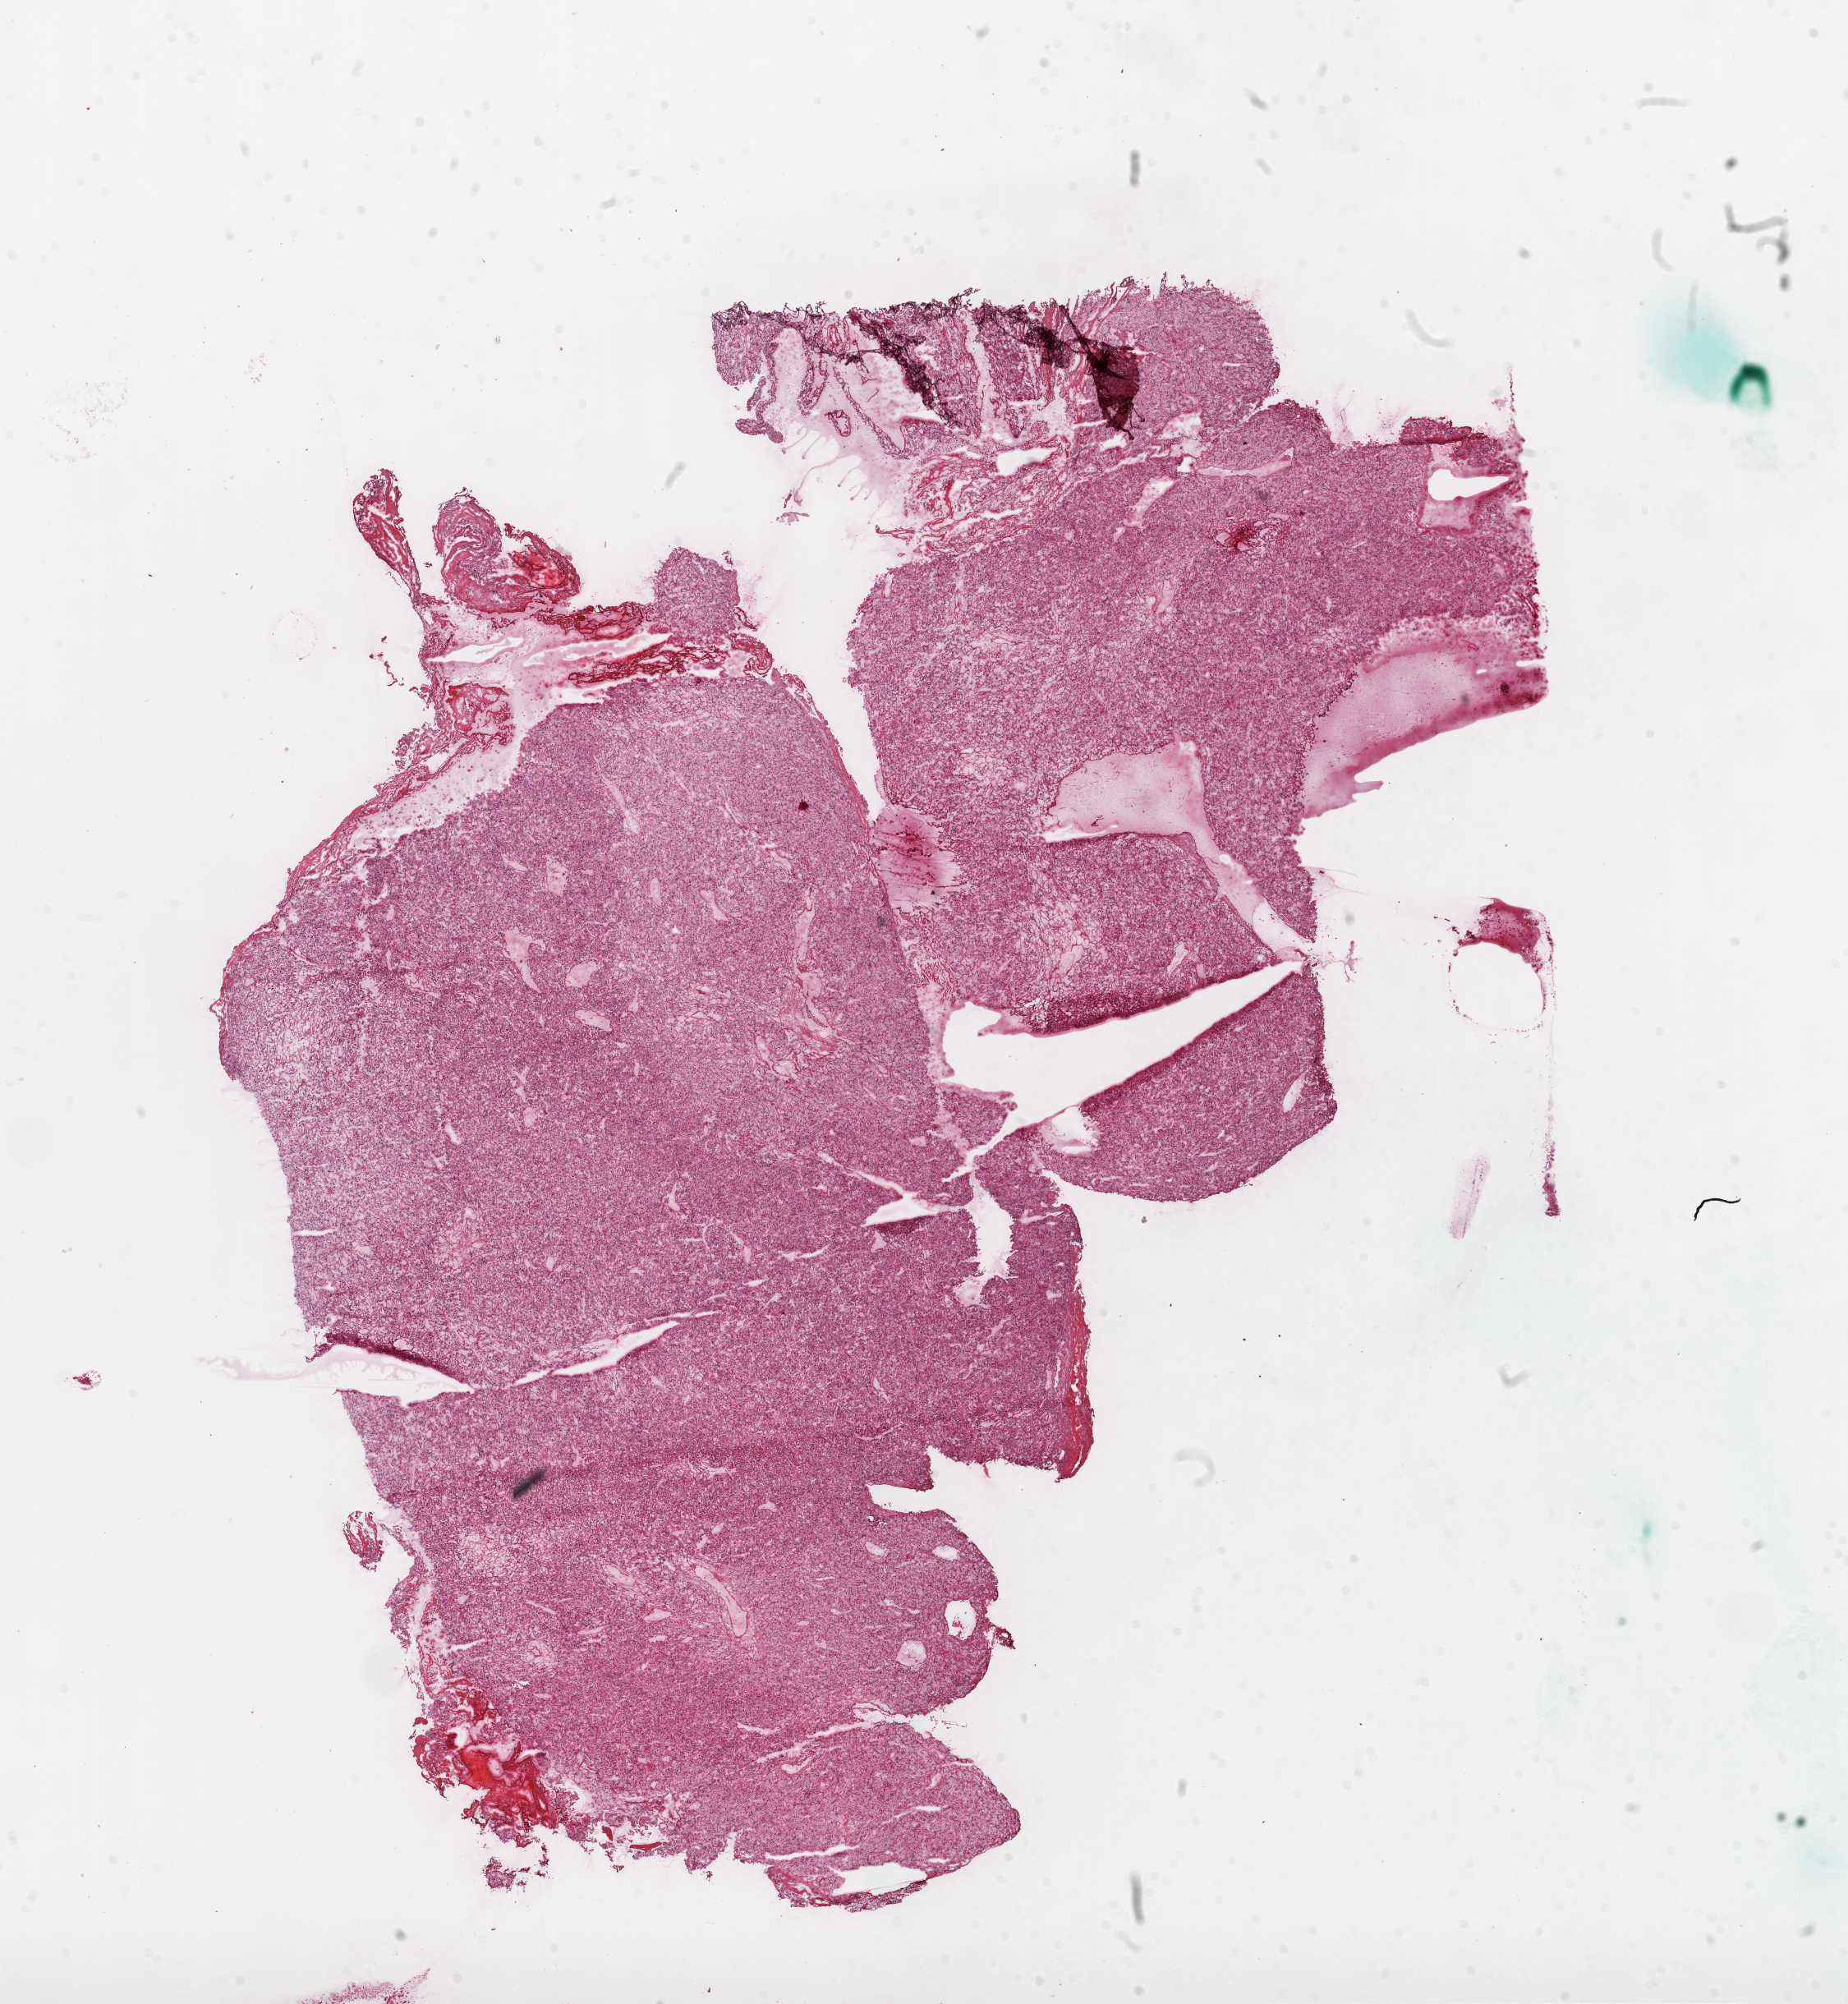
Digitized H&E-stained tissue section (whole slide) — a low-resolution overview of the entire scanned area, about 18.1 x 19.6 mm. Frozen section from the top of the tissue portion. Sample: primary tumour, kidney. Female, age 51 years at initial diagnosis. Histologic grade: G2 (moderately differentiated). Slide review estimates, as recorded: tumour cells 95%, tumour nuclei 85%, normal cells 0%, stromal cells 5%, necrosis 0%.
• AJCC pathologic stage: III
• histologic diagnosis: Clear cell adenocarcinoma, NOS
• lymph nodes positive (case pathology): 0 of 17 examined
• TNM: T3a N0 M0